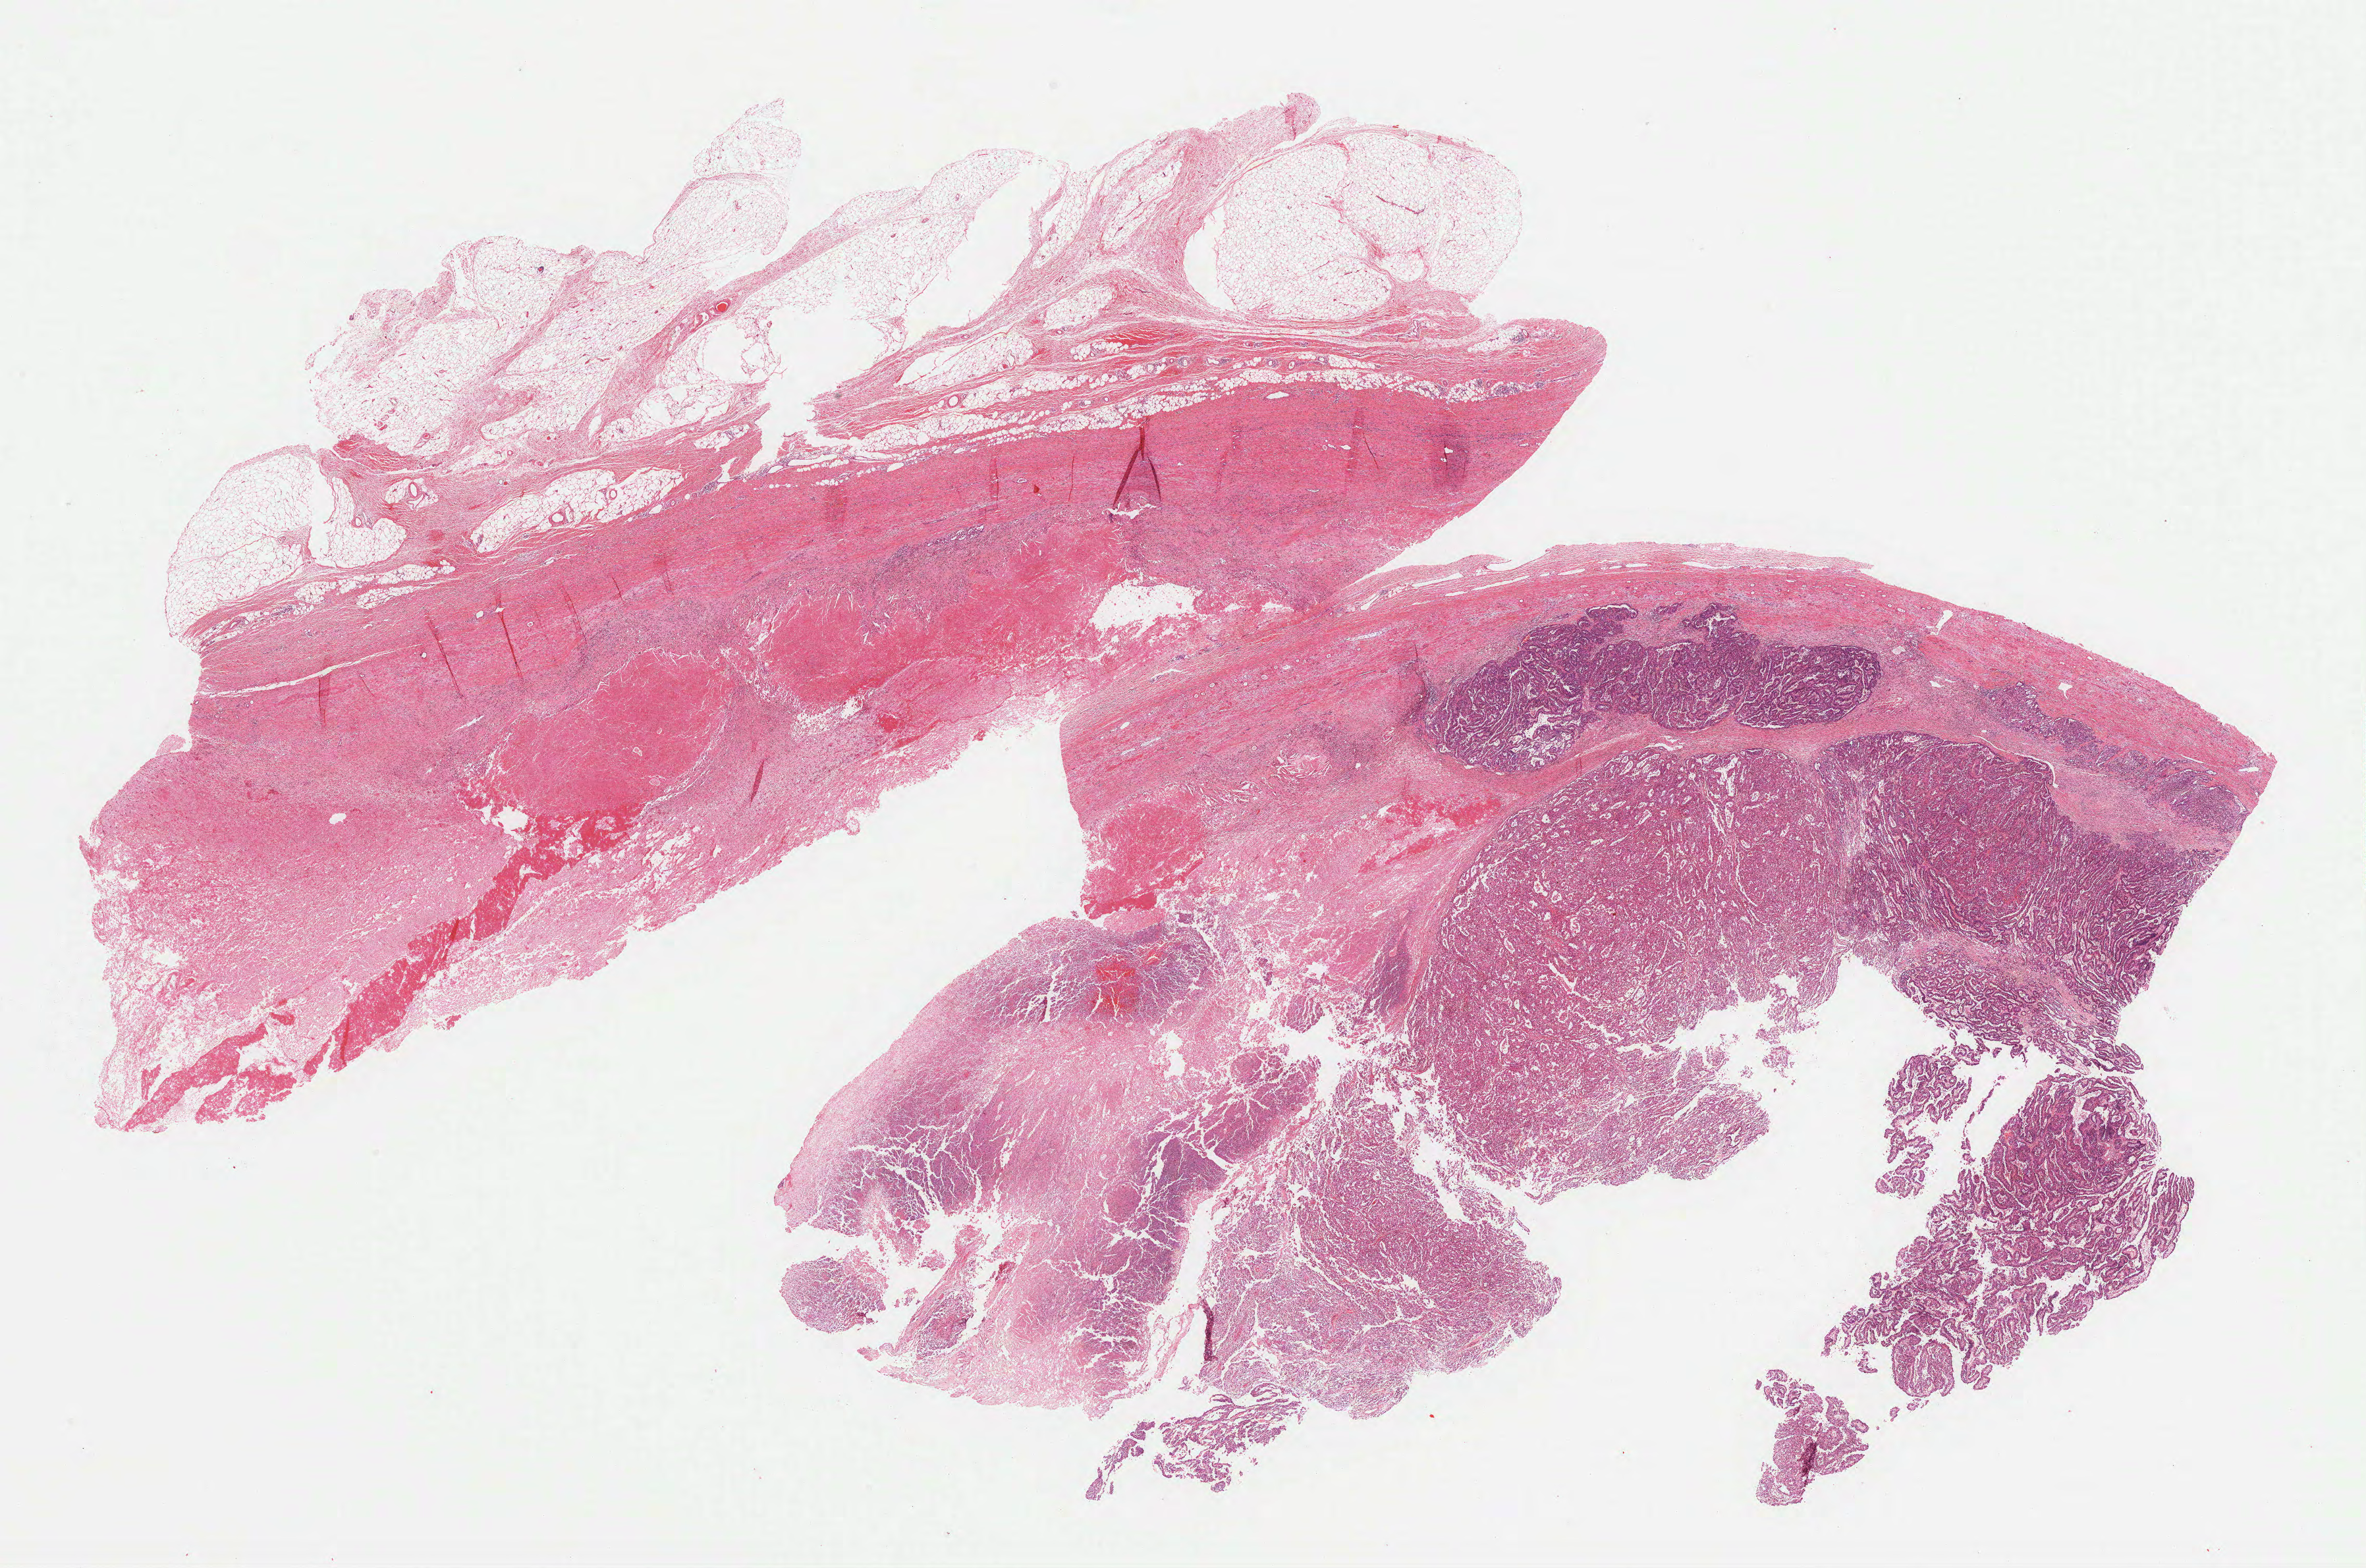
Whole-slide histology image, H&E-stained — low-resolution overview of the scanned area, about 28.5 x 18.9 mm (acquisition: 40x scan); FFPE section; primary tumour sample from the kidney. Female, age 60 years at initial diagnosis.
AJCC pathologic stage: III. Lymph nodes positive (case pathology): 2 of 7 examined. Histologic diagnosis: Papillary adenocarcinoma, NOS.